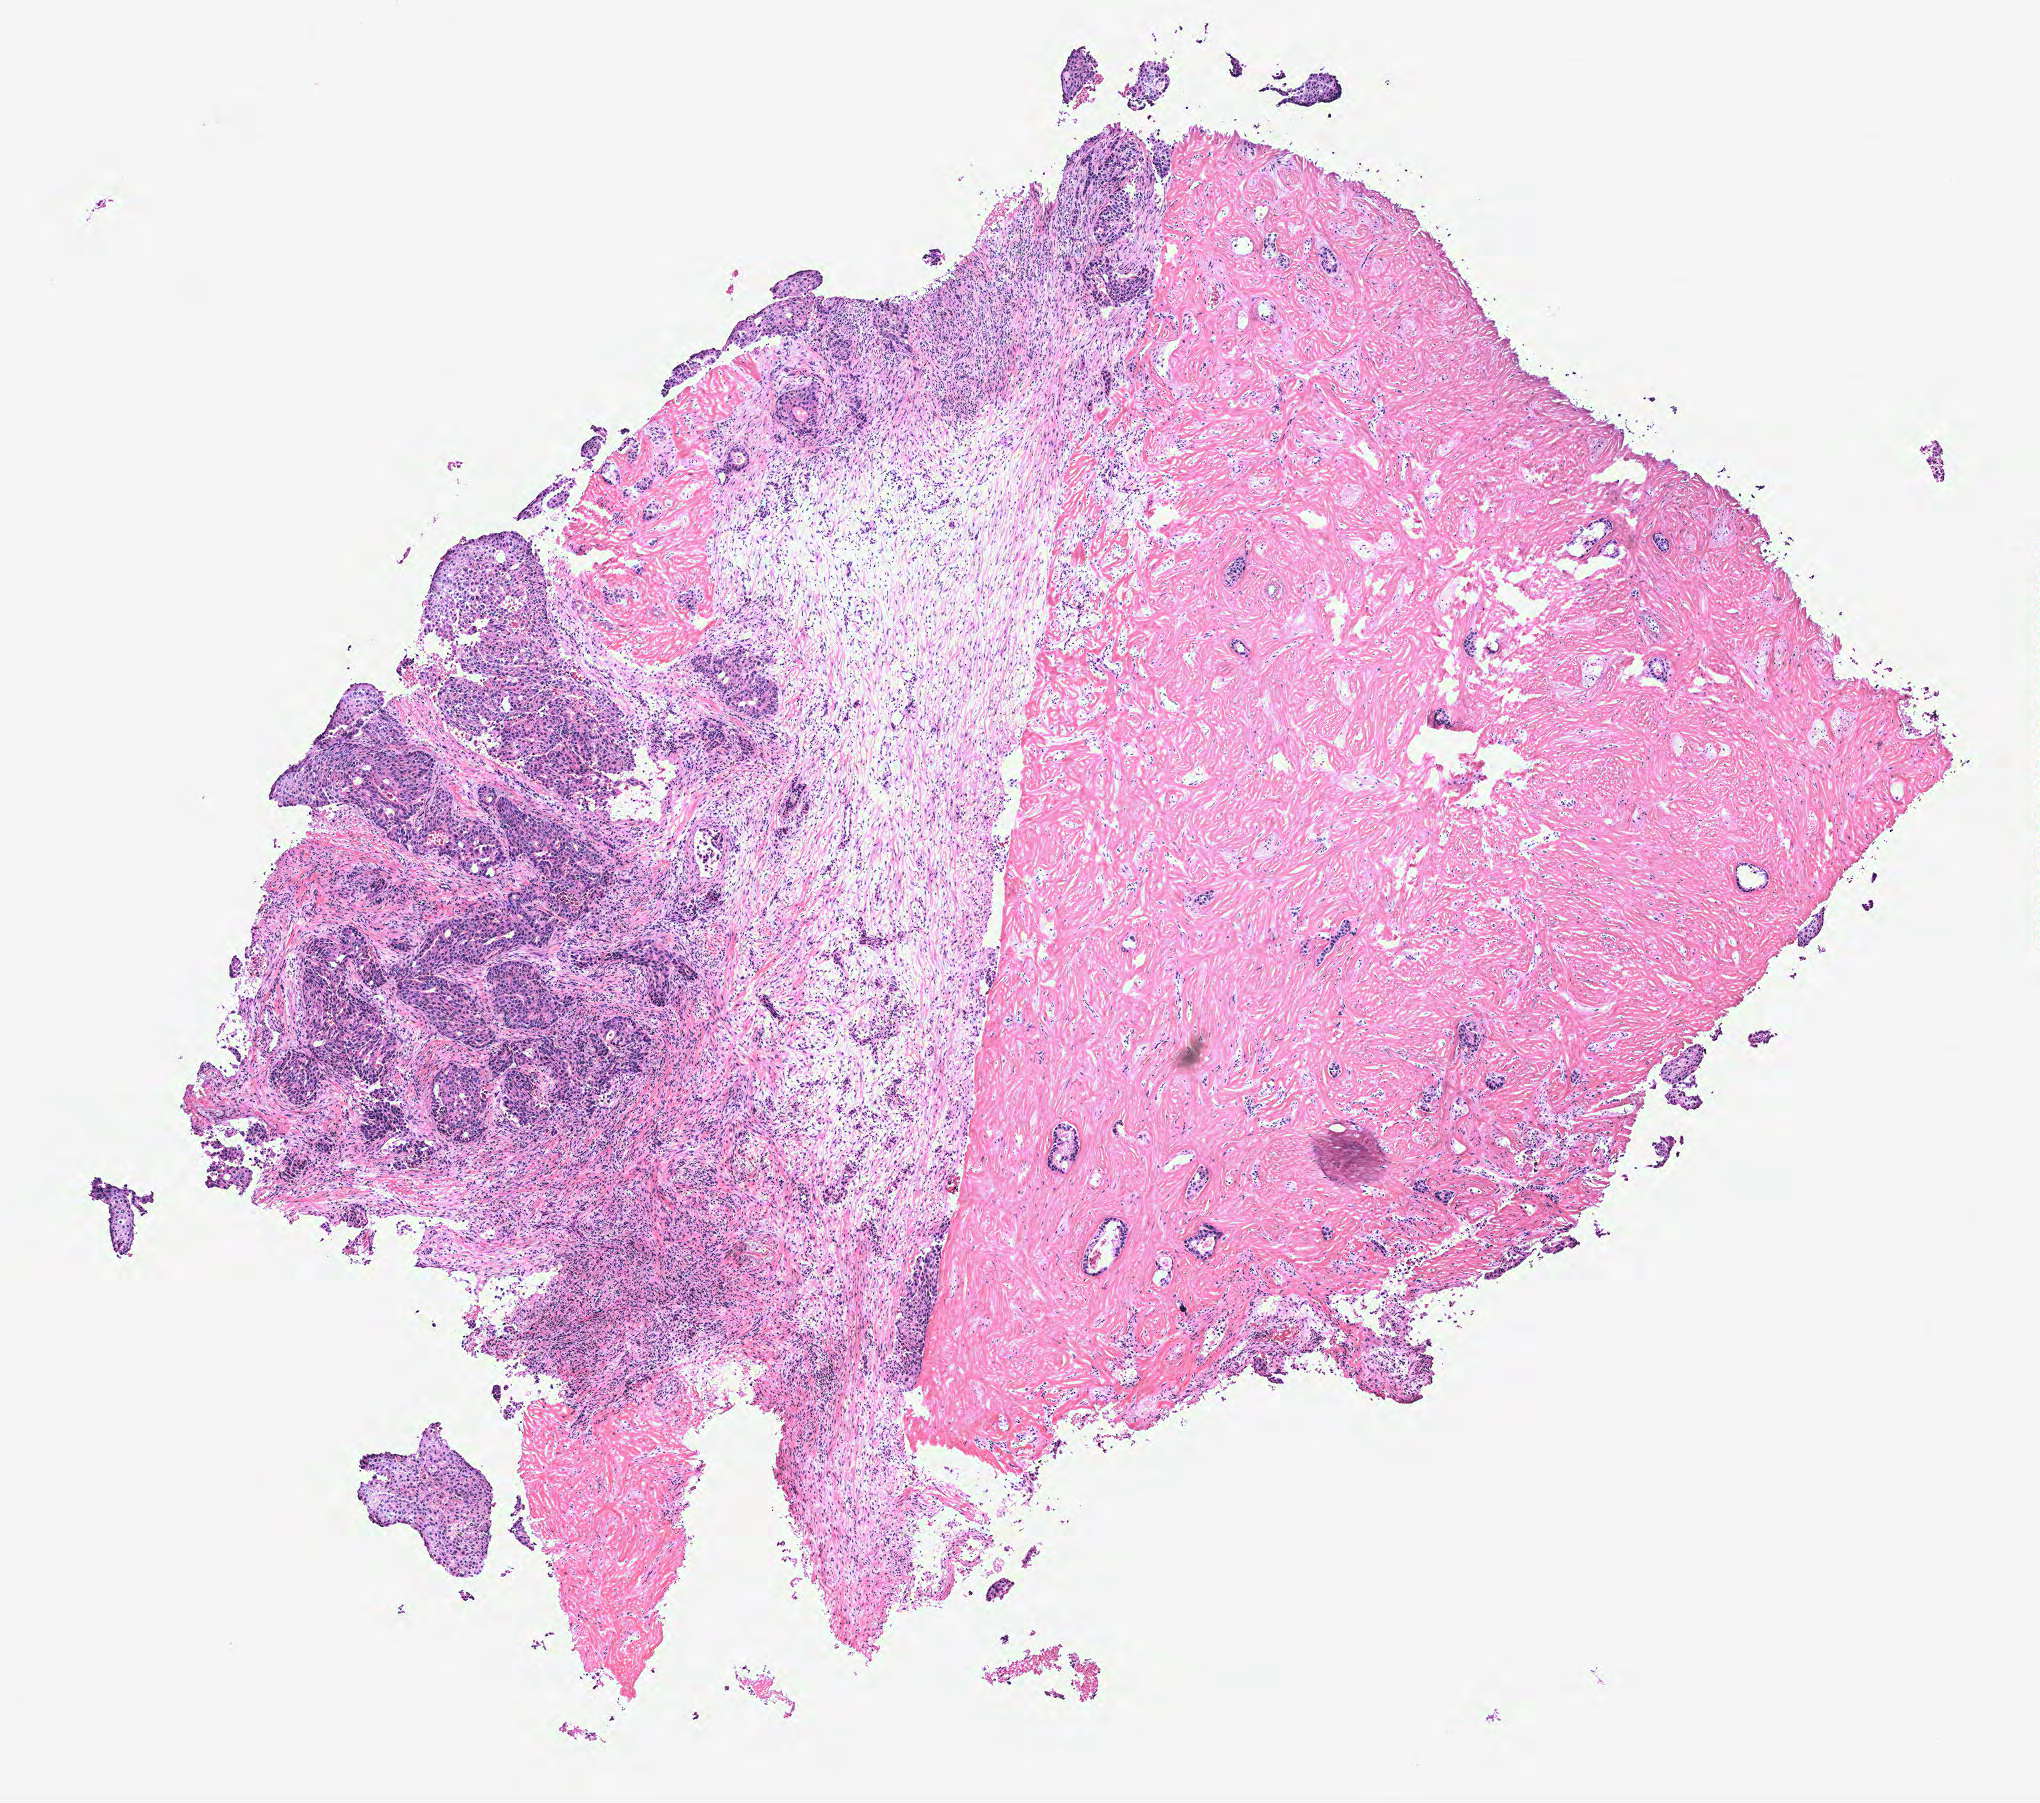
Whole-slide histology image, Hematoxylin and eosin (H&E) stained — shown as a low-resolution overview of the whole scanned area (about 8.2 x 7.2 mm). Breast, tumour tissue. 71-year-old female patient.
Diagnosis: Intraductal papillary carcinoma. AJCC pathologic stage: IIIB.